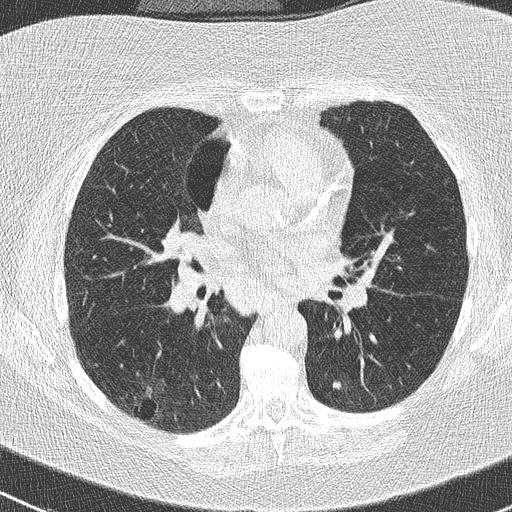
Low-dose screening chest CT, one axial slice. Slice 136 of 261 in the series (ordered by position). Reconstruction kernel B50f. 120 kVp. Lung window (W 1500 / L -600 HU). 512 × 512 image matrix, field of view 310 × 310 mm.
Annotated regions visible in this slice (outlined manually by an expert reader):
- lesion 1 (tumor, lower lobe of right lung): bounding box [x1, y1, x2, y2] px = [146, 387, 157, 411]